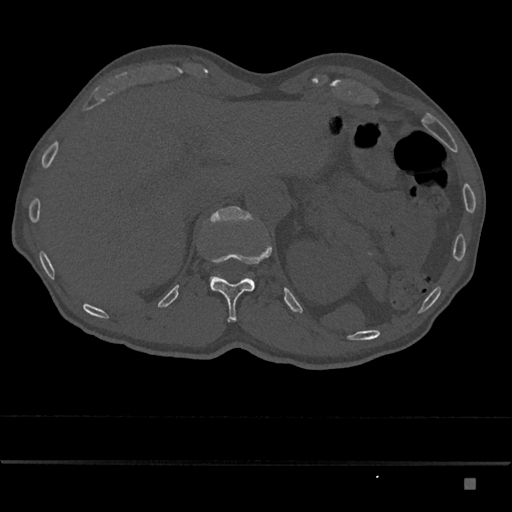
CT including the spine, one axial slice; slice 596 of 797 in the series (ordered by position); reconstruction kernel Br40s/3; 120 kVp; bone window (W 1800 / L 400 HU); 0.5 mm slice thickness; 512 × 512 image matrix. Male patient, age 72 years. From the clinical record (not read from this slice): primary cancer: prostate.
Outlined on this slice (semi-automatic segmentation, software-assisted and operator-edited):
- L1 vertebra: bounding box [x1, y1, x2, y2] px = [204, 207, 255, 288]
- T12 vertebra: [210, 246, 272, 322]